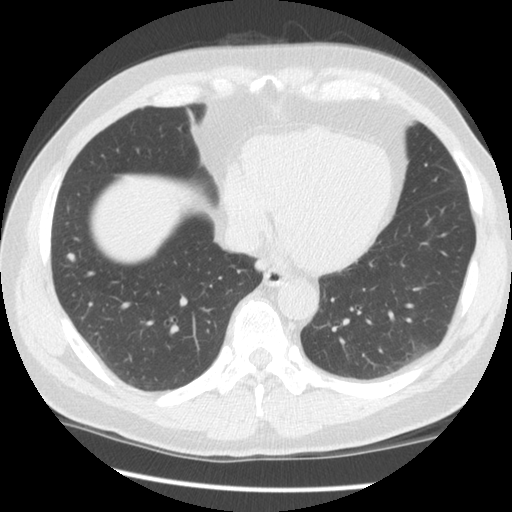
Axial slice from a low-dose chest CT screening exam. Second screening round (one year after baseline). Lung window (W 1500 / L -600 HU). Slice 53 of 135 in the series. 512 × 512 image matrix. Male, age 61 years at enrolment.
Expert reader's lesion annotation, bounding box <50,243,86,278> (left, top, right, bottom; pixels). Screening reader's record for this exam (one nodule recorded; not confirmed to be the boxed lesion): non-calcified nodule or mass ≥4 mm, right lower lobe, 5 × 4 mm, smooth margins, soft tissue attenuation, pre-existing on the prior screen: no. Later outcome: lung cancer diagnosed 311 days after this screen — small cell carcinoma, NOS, right hilum, undifferentiated (G4), stage IV (AJCC 6th edition), 140 mm at pathology.